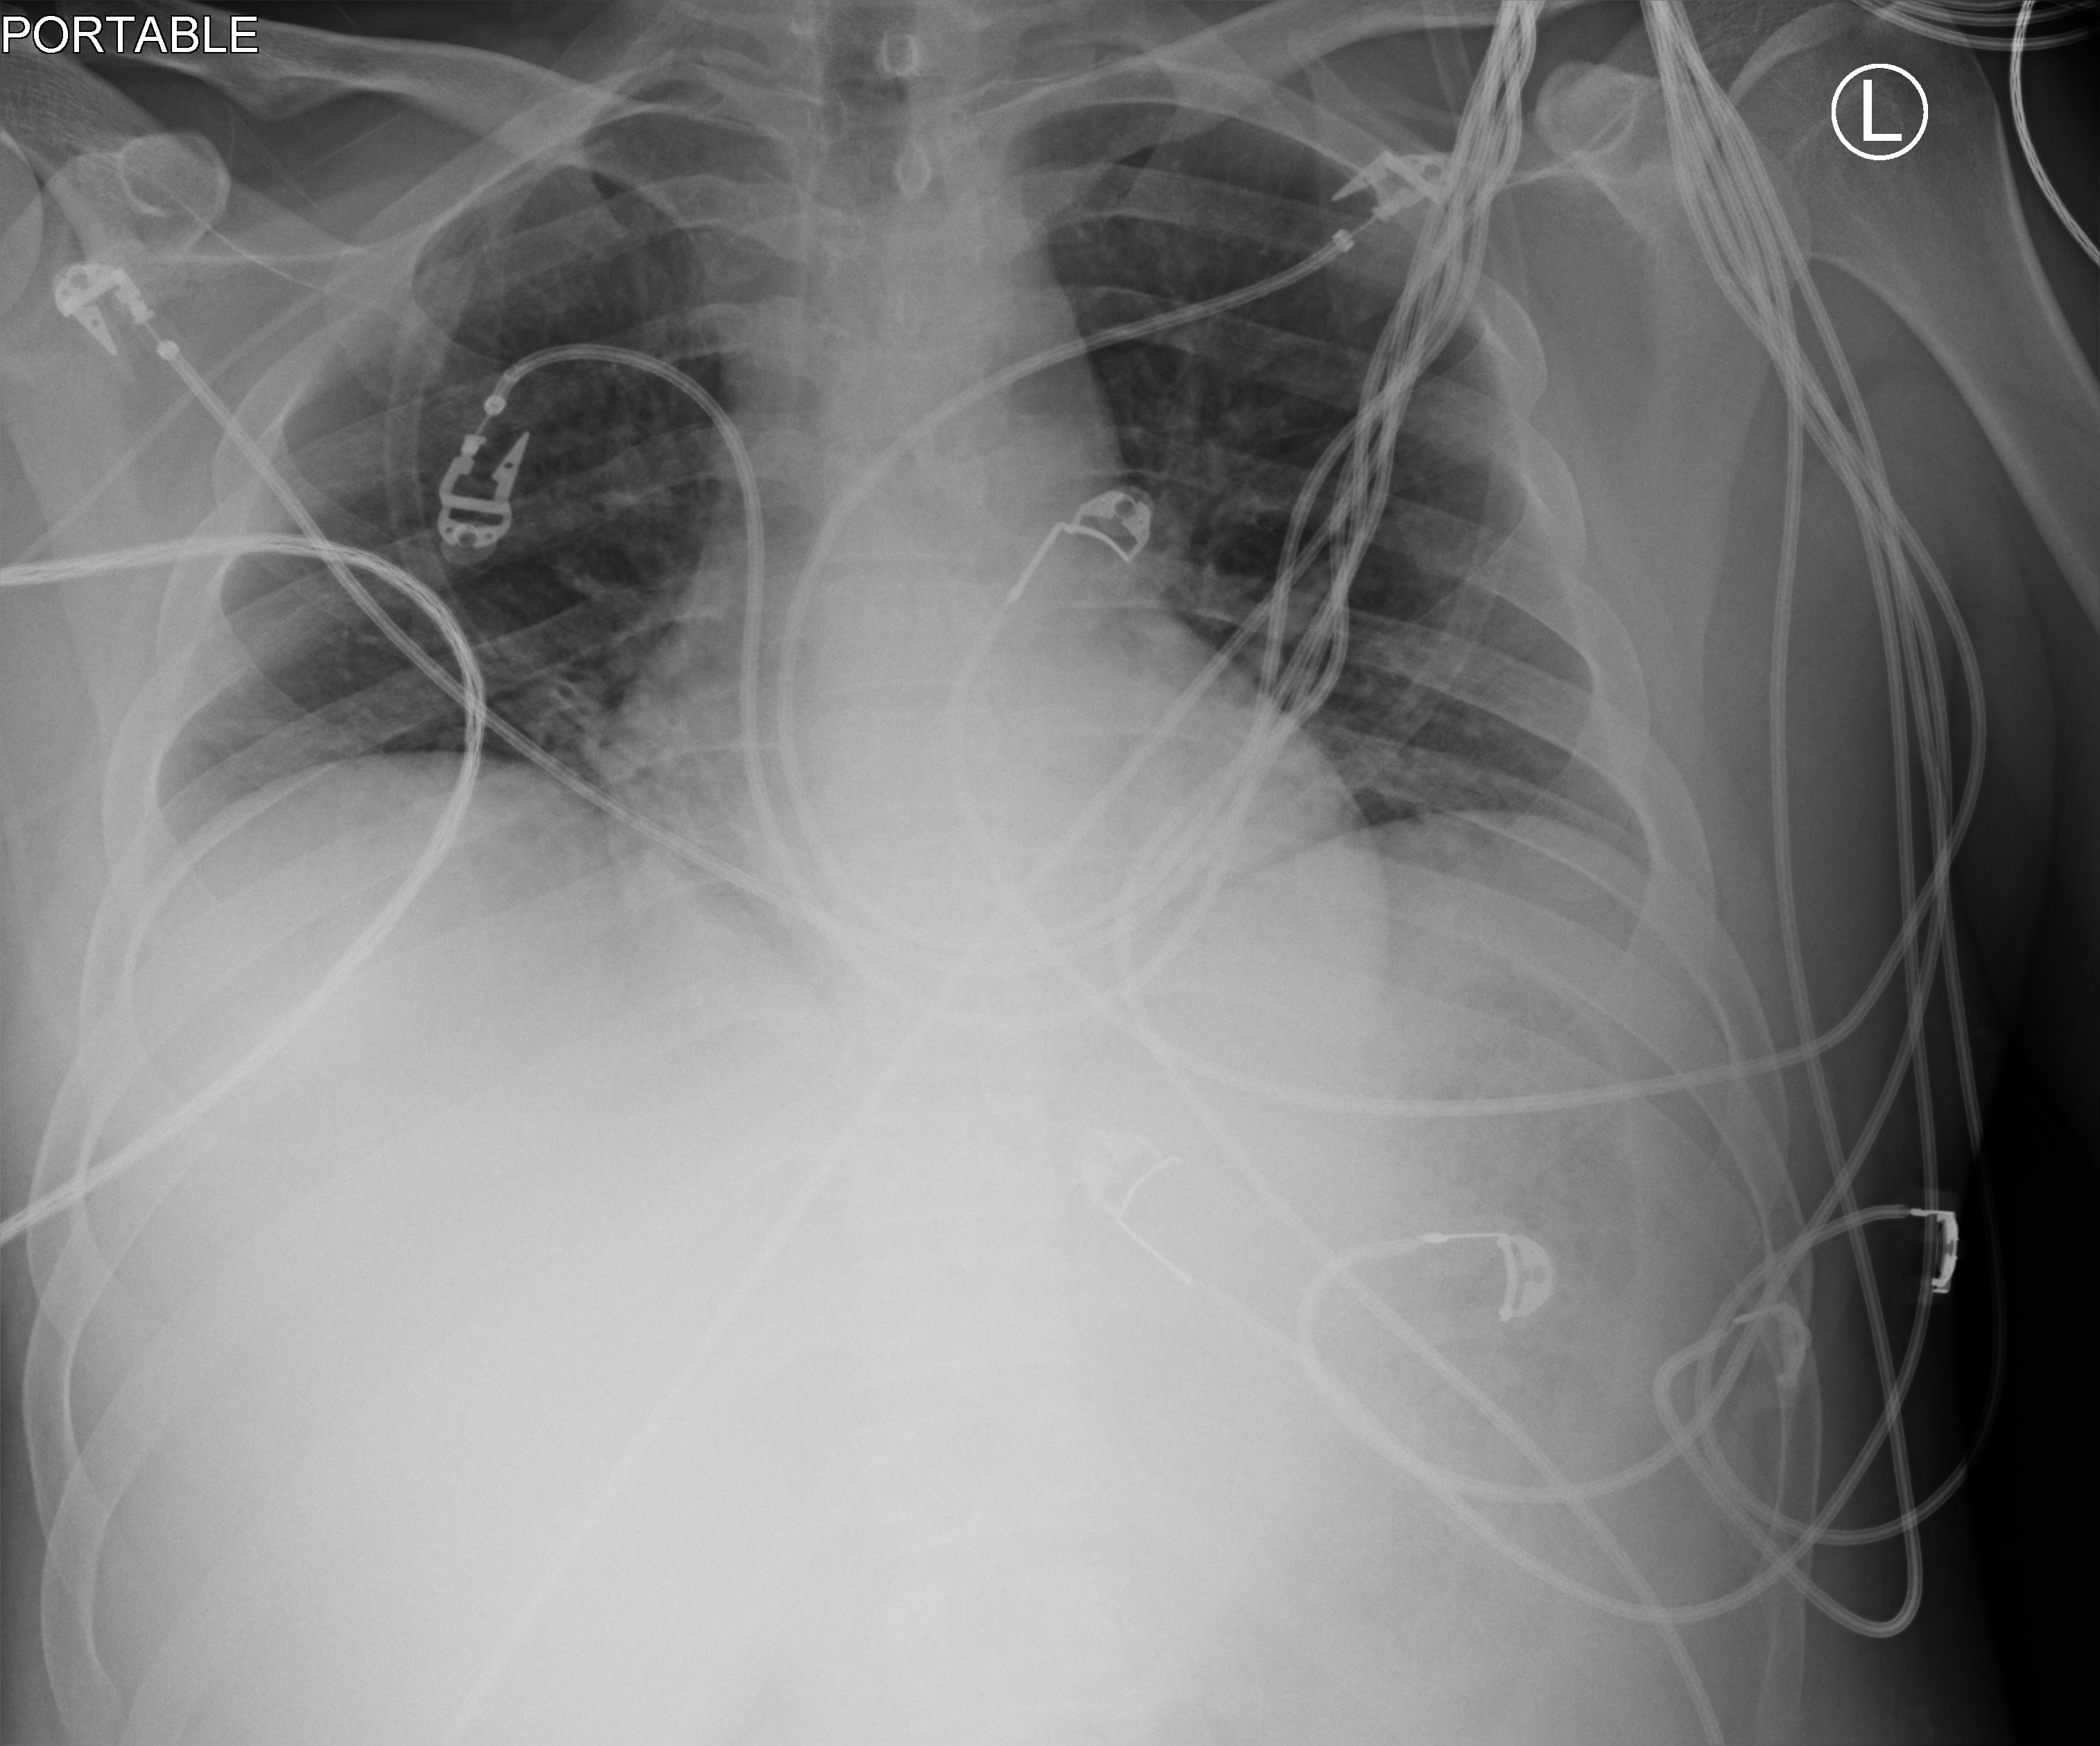
Portable chest radiograph. Male patient hospitalised with COVID-19, age 18–59 years.
Hospital-stay facts (about this admission, not read from this image; timing relative to this image not recorded): mechanically ventilated during this hospital stay: yes.